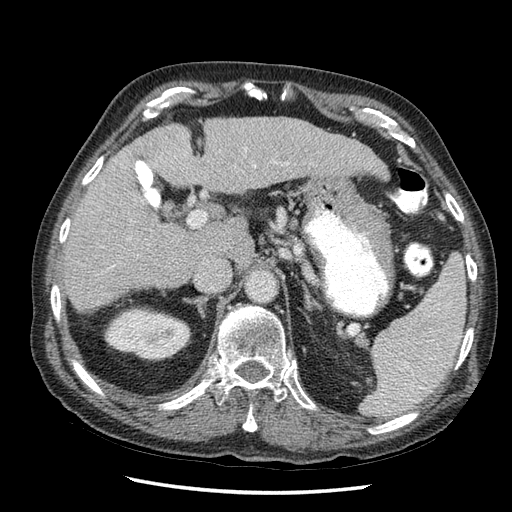
Contrast-enhanced abdominal CT (liver protocol), one axial slice. Position 26 of 67 along the scan axis. Reconstruction kernel STANDARD. Soft-tissue window (W 400 / L 40 HU). 512 × 512 image matrix. From the clinical record (not read from this slice): diagnosis: hepatocellular carcinoma (patient treated with transarterial chemoembolisation; whether this scan precedes or follows treatment is not stated here); TNM stage (as recorded): Stage-I; Child-Pugh class: A; tumour nodularity: uninodular.
Annotated regions visible in this slice (semi-automatically segmented with operator editing):
- liver parenchyma outside the tumour (the mass and vessels are separate outlines, so this box may not span the whole liver): bounding box <60,118,372,312> (left, top, right, bottom; pixels)
- liver vessels: <126,147,243,245>